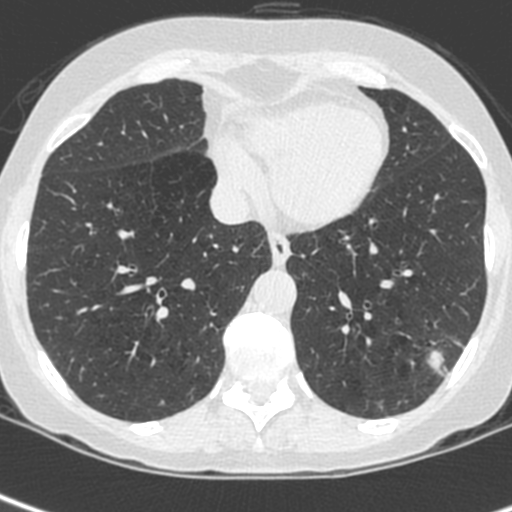
Low-dose screening chest CT, axial slice; baseline annual screen; lung window (W 1500 / L -600 HU); 120 kVp; 512 × 512 image matrix. Female participant, aged 56 years at enrolment. Current smoker at enrolment.
Expert reader's lesion annotation, bounding box <411,332,471,391> (left, top, right, bottom; pixels). The exam's reader record, not a measurement of the box and not confirmed to be the same lesion: non-calcified nodule or mass ≥4 mm, left lower lobe, 37 × 29 mm, spiculated (stellate) margins, ground glass attenuation. Official screen result: positive, change unspecified: nodule(s) >= 4 mm or enlarging nodule(s), mass(es), or other non-specific abnormalities suspicious for lung cancer.